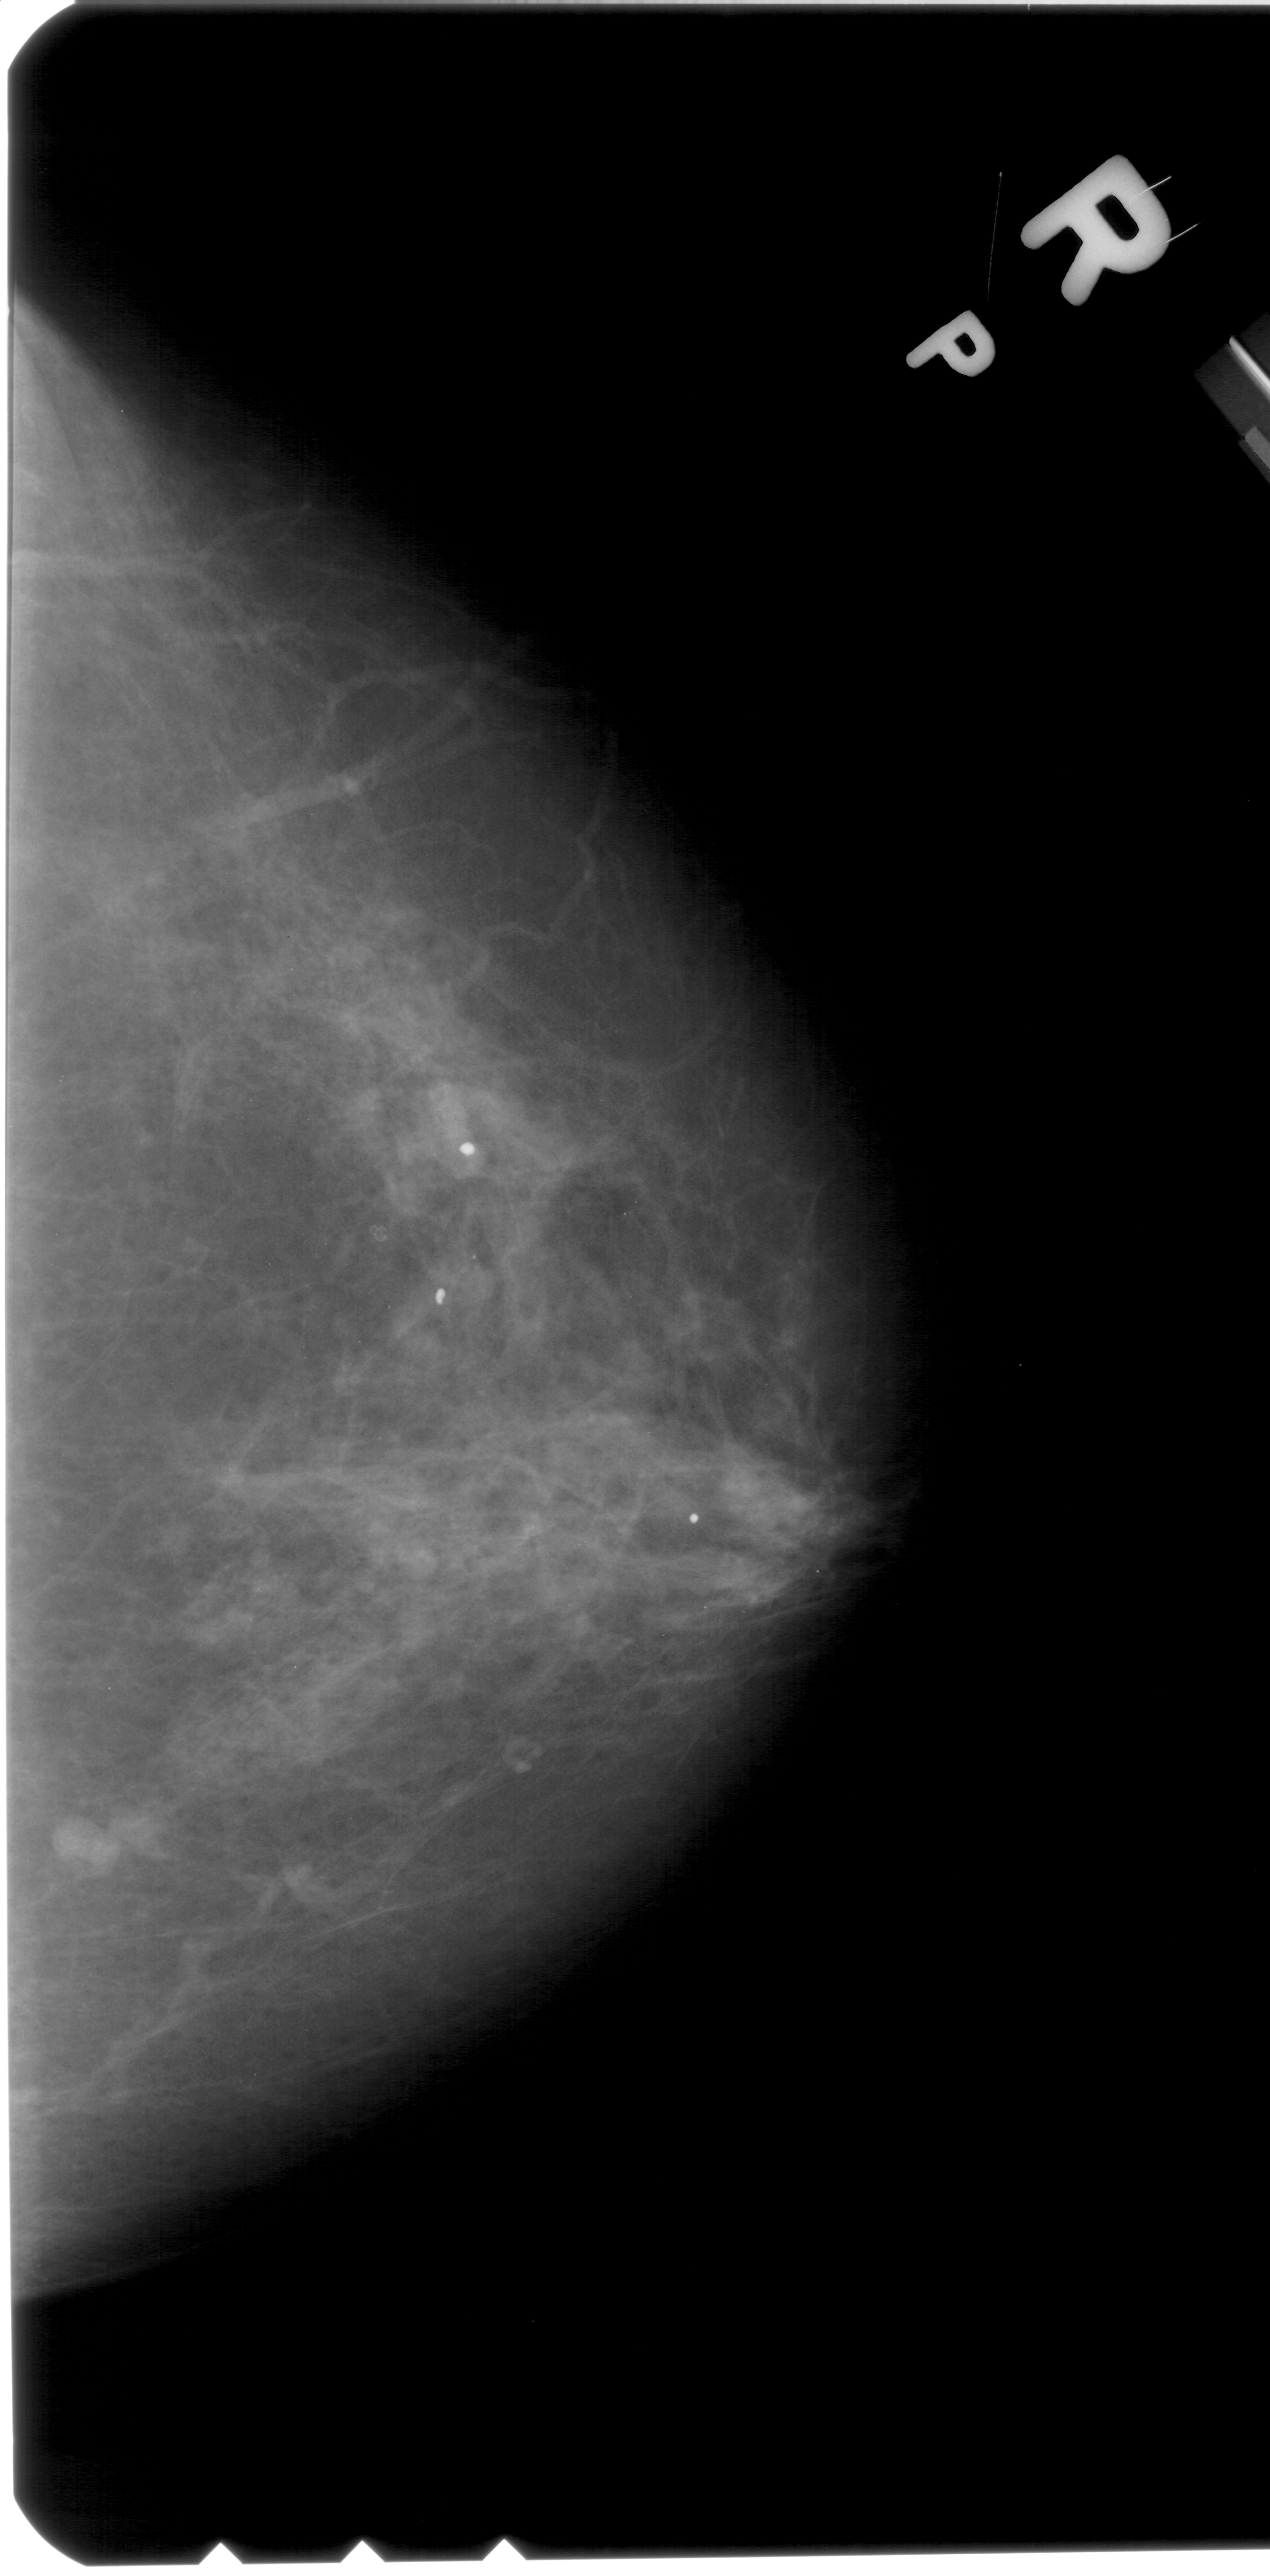
Digitized screen-film mammogram; right breast; craniocaudal (CC) view; breast composition: heterogeneously dense (BI-RADS density category 3 of 4); 1270 × 2576 image matrix.
Marked abnormalities (boxes around the expert regions of interest):
- mass, shape lobulated, margins circumscribed; BI-RADS assessment category 4; subtlety rating 4 on a 1 (subtle) to 5 (obvious) scale; pathology (as recorded): benign: bounding box <51,1812,135,1887> (left, top, right, bottom; pixels)